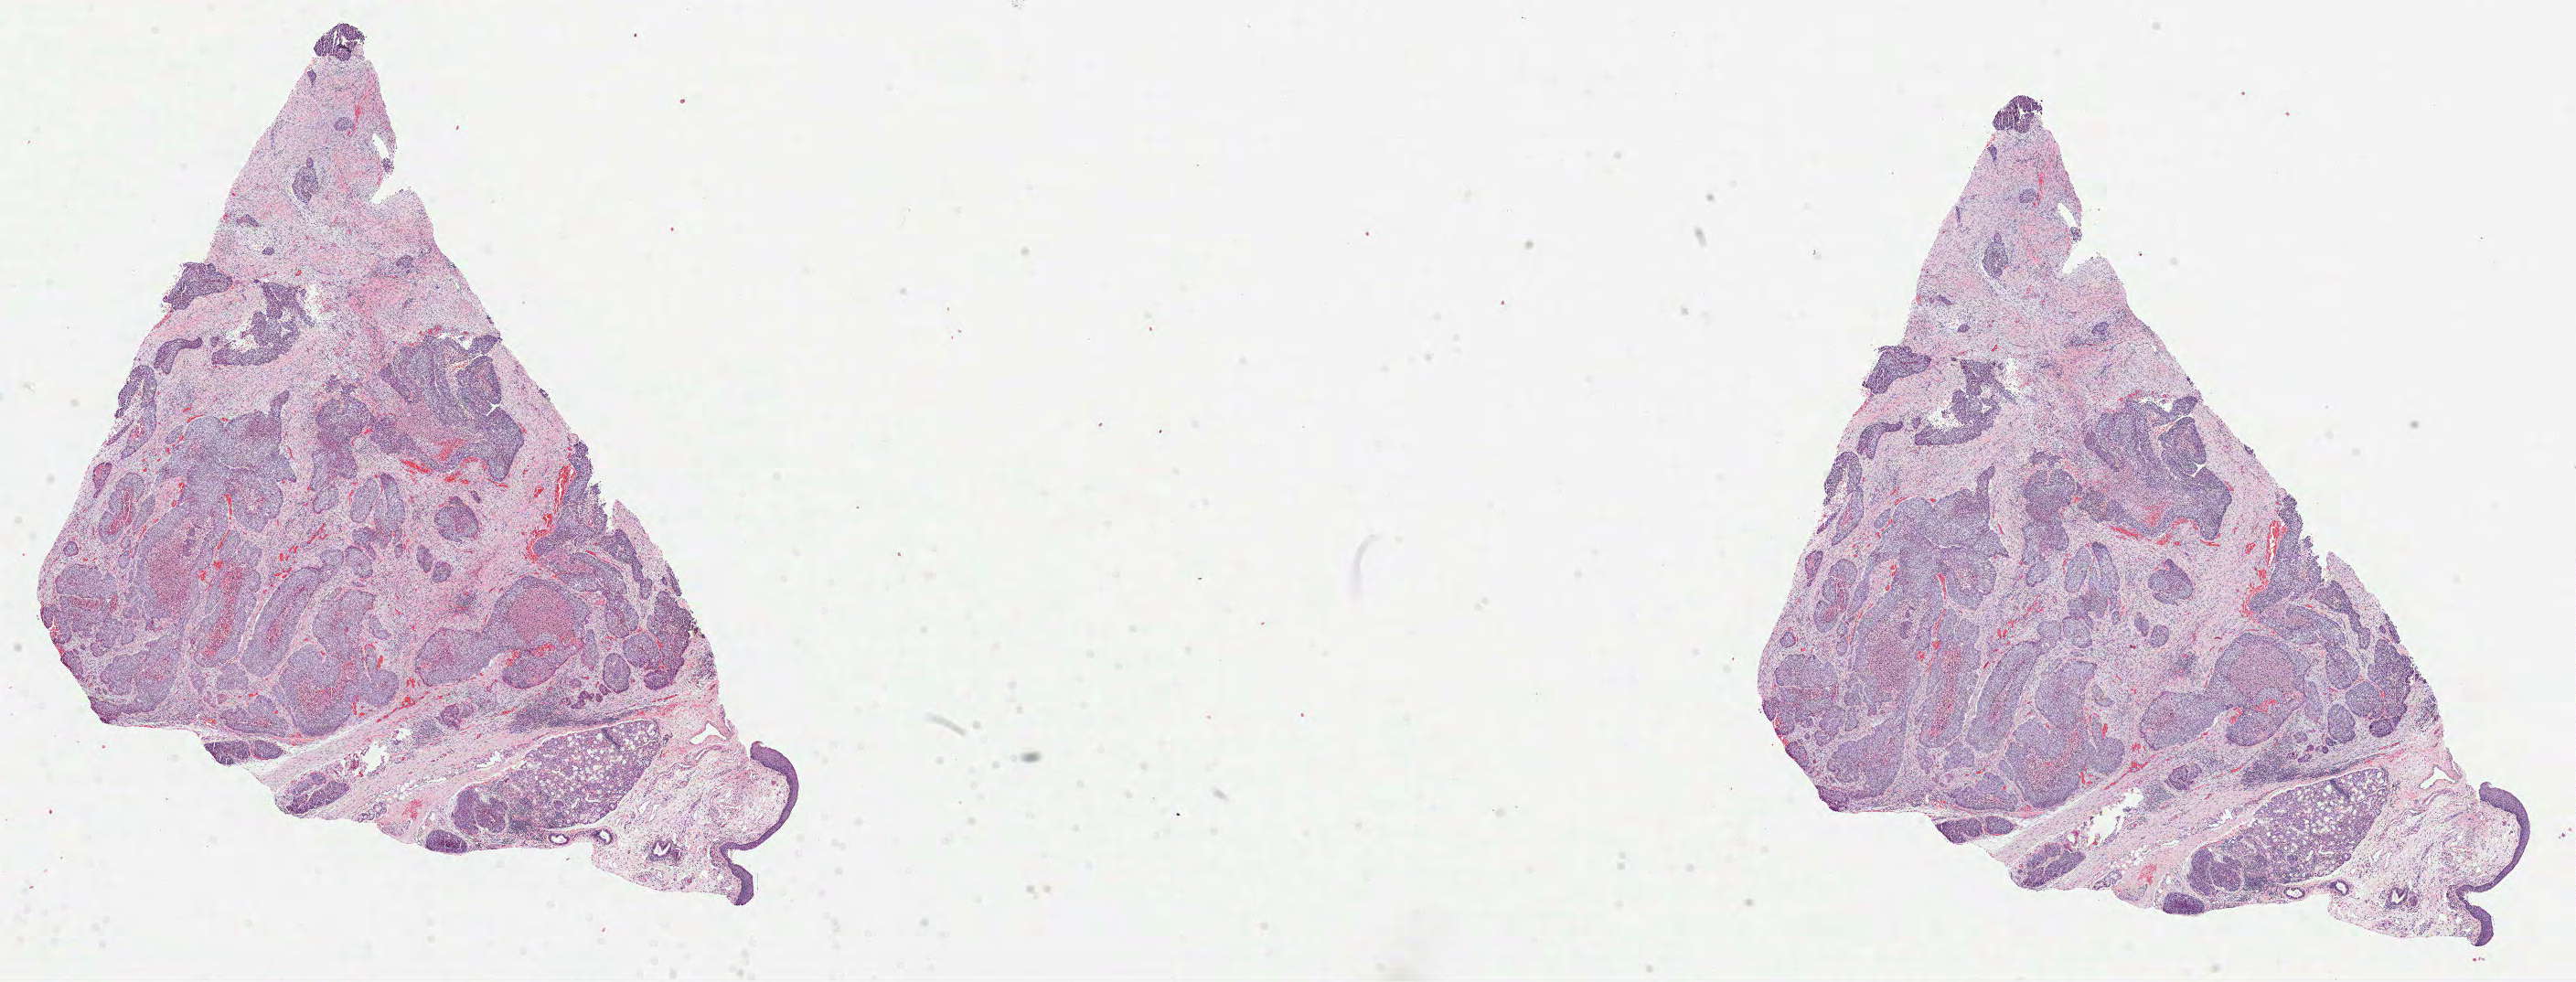
H&E whole-slide image — whole scanned area (about 22.7 x 8.7 mm, from a 40x scan) shown as a low-resolution overview; formalin-fixed paraffin-embedded (FFPE) diagnostic section; sample: primary tumour, head and neck. Male patient; age at initial diagnosis 66 years. Histologic grade: G3 (poorly differentiated).
Lymph nodes positive (case pathology): 2 of 25 examined. AJCC pathologic stage: IVA (7th edition). Histologic diagnosis: Squamous cell carcinoma, NOS.